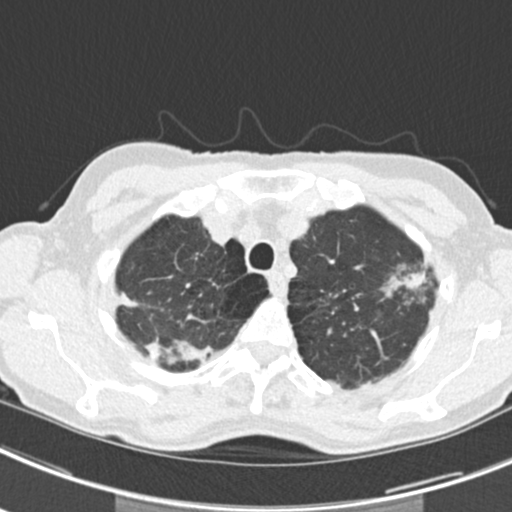
Axial slice from a low-dose chest CT screening exam, second screening round (one year after baseline), lung window (W 1500 / L -600 HU), 120 kVp, slice 38 of 219 in the series. Female participant, aged 63 years at enrolment.
Lesion marked by an expert reader, bounding box <375,249,439,310> (left, top, right, bottom; pixels). The screening reader recorded 9 non-calcified nodules or masses ≥4 mm on this exam (left upper lobe, right upper lobe, left upper lobe, left lower lobe, right middle lobe, left lower lobe, left lower lobe, right lower lobe, right lower lobe); which of them this box marks is not recorded.